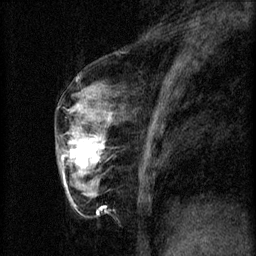
Breast MRI (dynamic contrast-enhanced), one sagittal slice. Position 25 of 60 along the scan axis. 3 images stored at this slice position (order not interpretable as contrast timing). 1.5 T. TE 4.2 ms, TR 8.2 ms. 2 mm slice thickness. 256 × 256 image matrix. Patient: female, 56 years.
Annotated regions visible in this slice (semi-automatically segmented with operator editing):
- analysis volume of interest (the breast-tissue region the enhancement analysis was run in; not a lesion): box from (x=60, y=124) to (x=114, y=179) px
- tumour enhancement mask (voxels above the 70 % enhancement threshold inside the analysis volume of interest): (x=63, y=134)–(x=105, y=169)